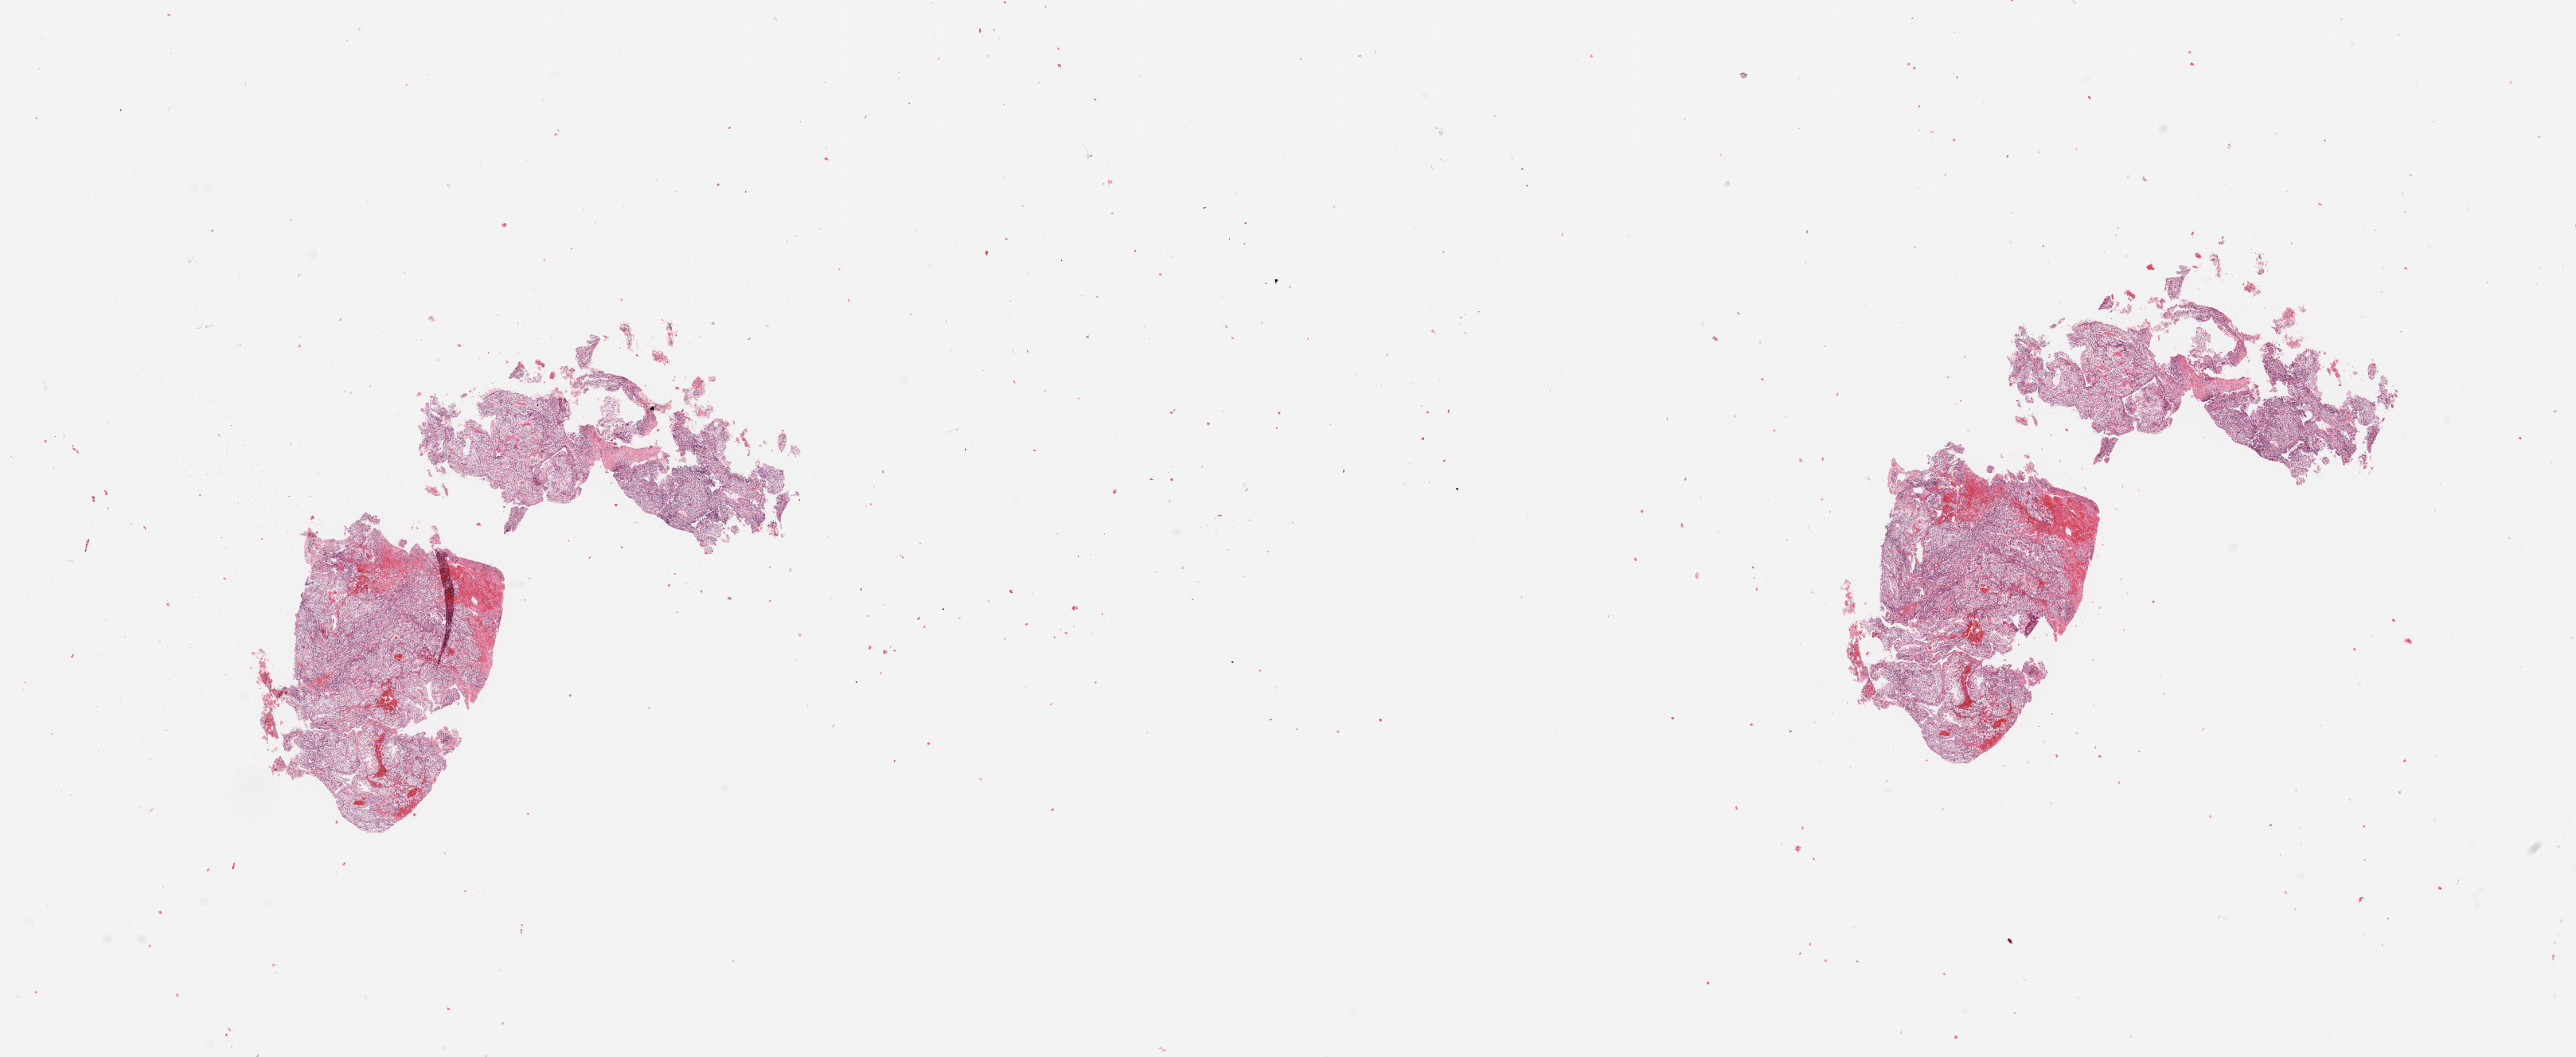
H&E-stained whole-slide image, shown as a low-resolution overview of the whole scanned area (about 25.6 x 10.5 mm, from a 20x scan). Tumour tissue sample, sampled site: kidney. Patient: male, age 44 years. Histologic grade: G2 (moderately differentiated). Slide review estimates, as recorded: tumour nuclei 90%, necrosis 5%.
- AJCC pathologic stage: I
- histologic diagnosis: Renal cell carcinoma, NOS
- primary tumour site (as recorded): lower pole